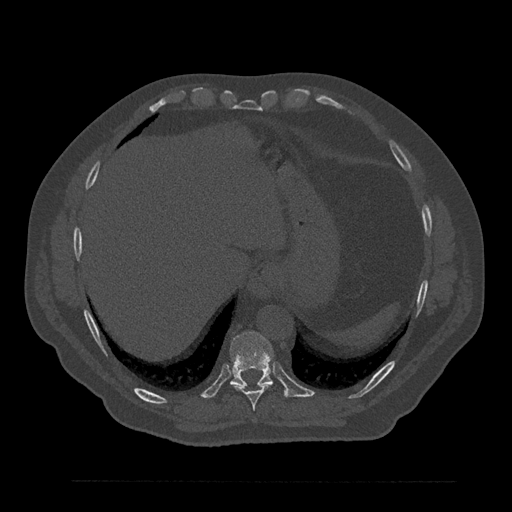
CT including the spine, one axial slice; reconstruction kernel Br40s/3; bone window (W 1800 / L 400 HU); 0.5 mm slice thickness; 512 × 512 image matrix, field of view 430 × 430 mm. Male patient, age 61 years. Case-level facts recorded for this patient, not image findings: primary cancer: prostate.
Outlined on this slice (semi-automatic segmentation, software-assisted and operator-edited):
- T10 vertebra: bounding box [x1, y1, x2, y2] px = [230, 331, 274, 386]
- T9 vertebra: [231, 383, 273, 410]